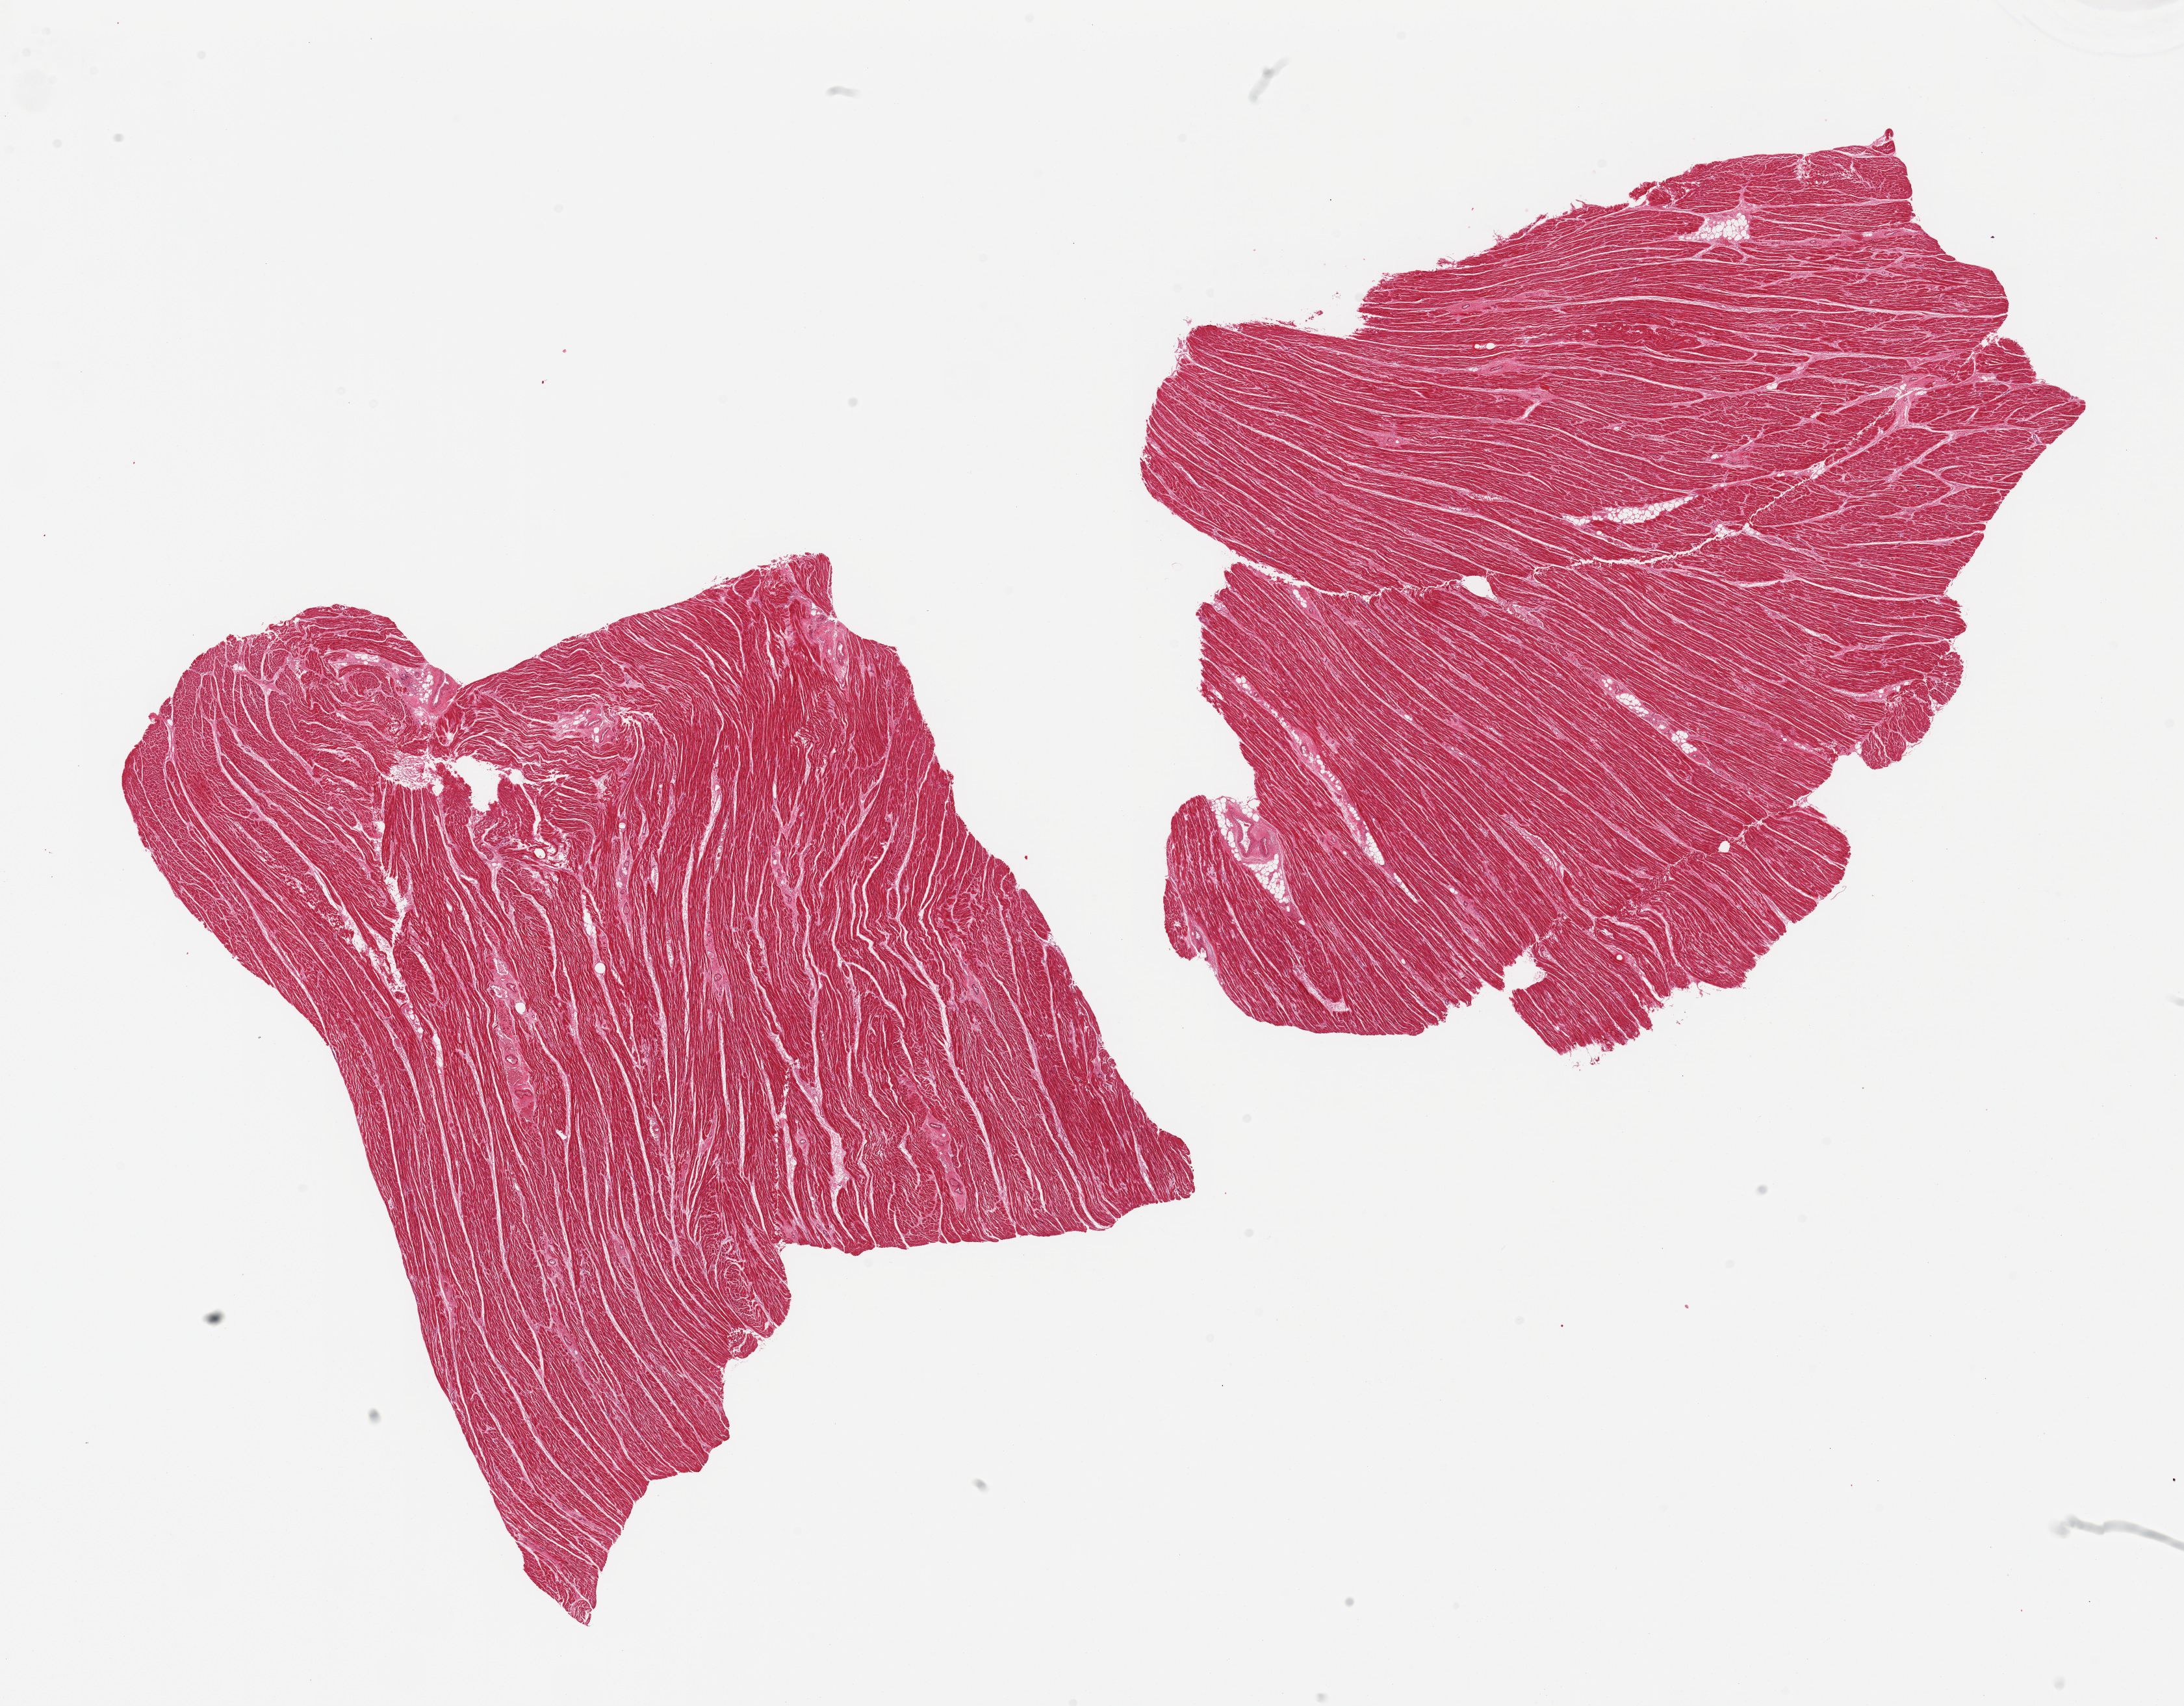
Digitized H&E-stained section, brightfield, shown as a low-resolution overview of the whole scanned area (about 26.6 x 20.8 mm, acquisition: 20x scan). PAXgene-fixed, paraffin-embedded tissue. Target tissue: heart. Tissue donor sample.
Reviewer comment on this tissue sample: 2 pieces.